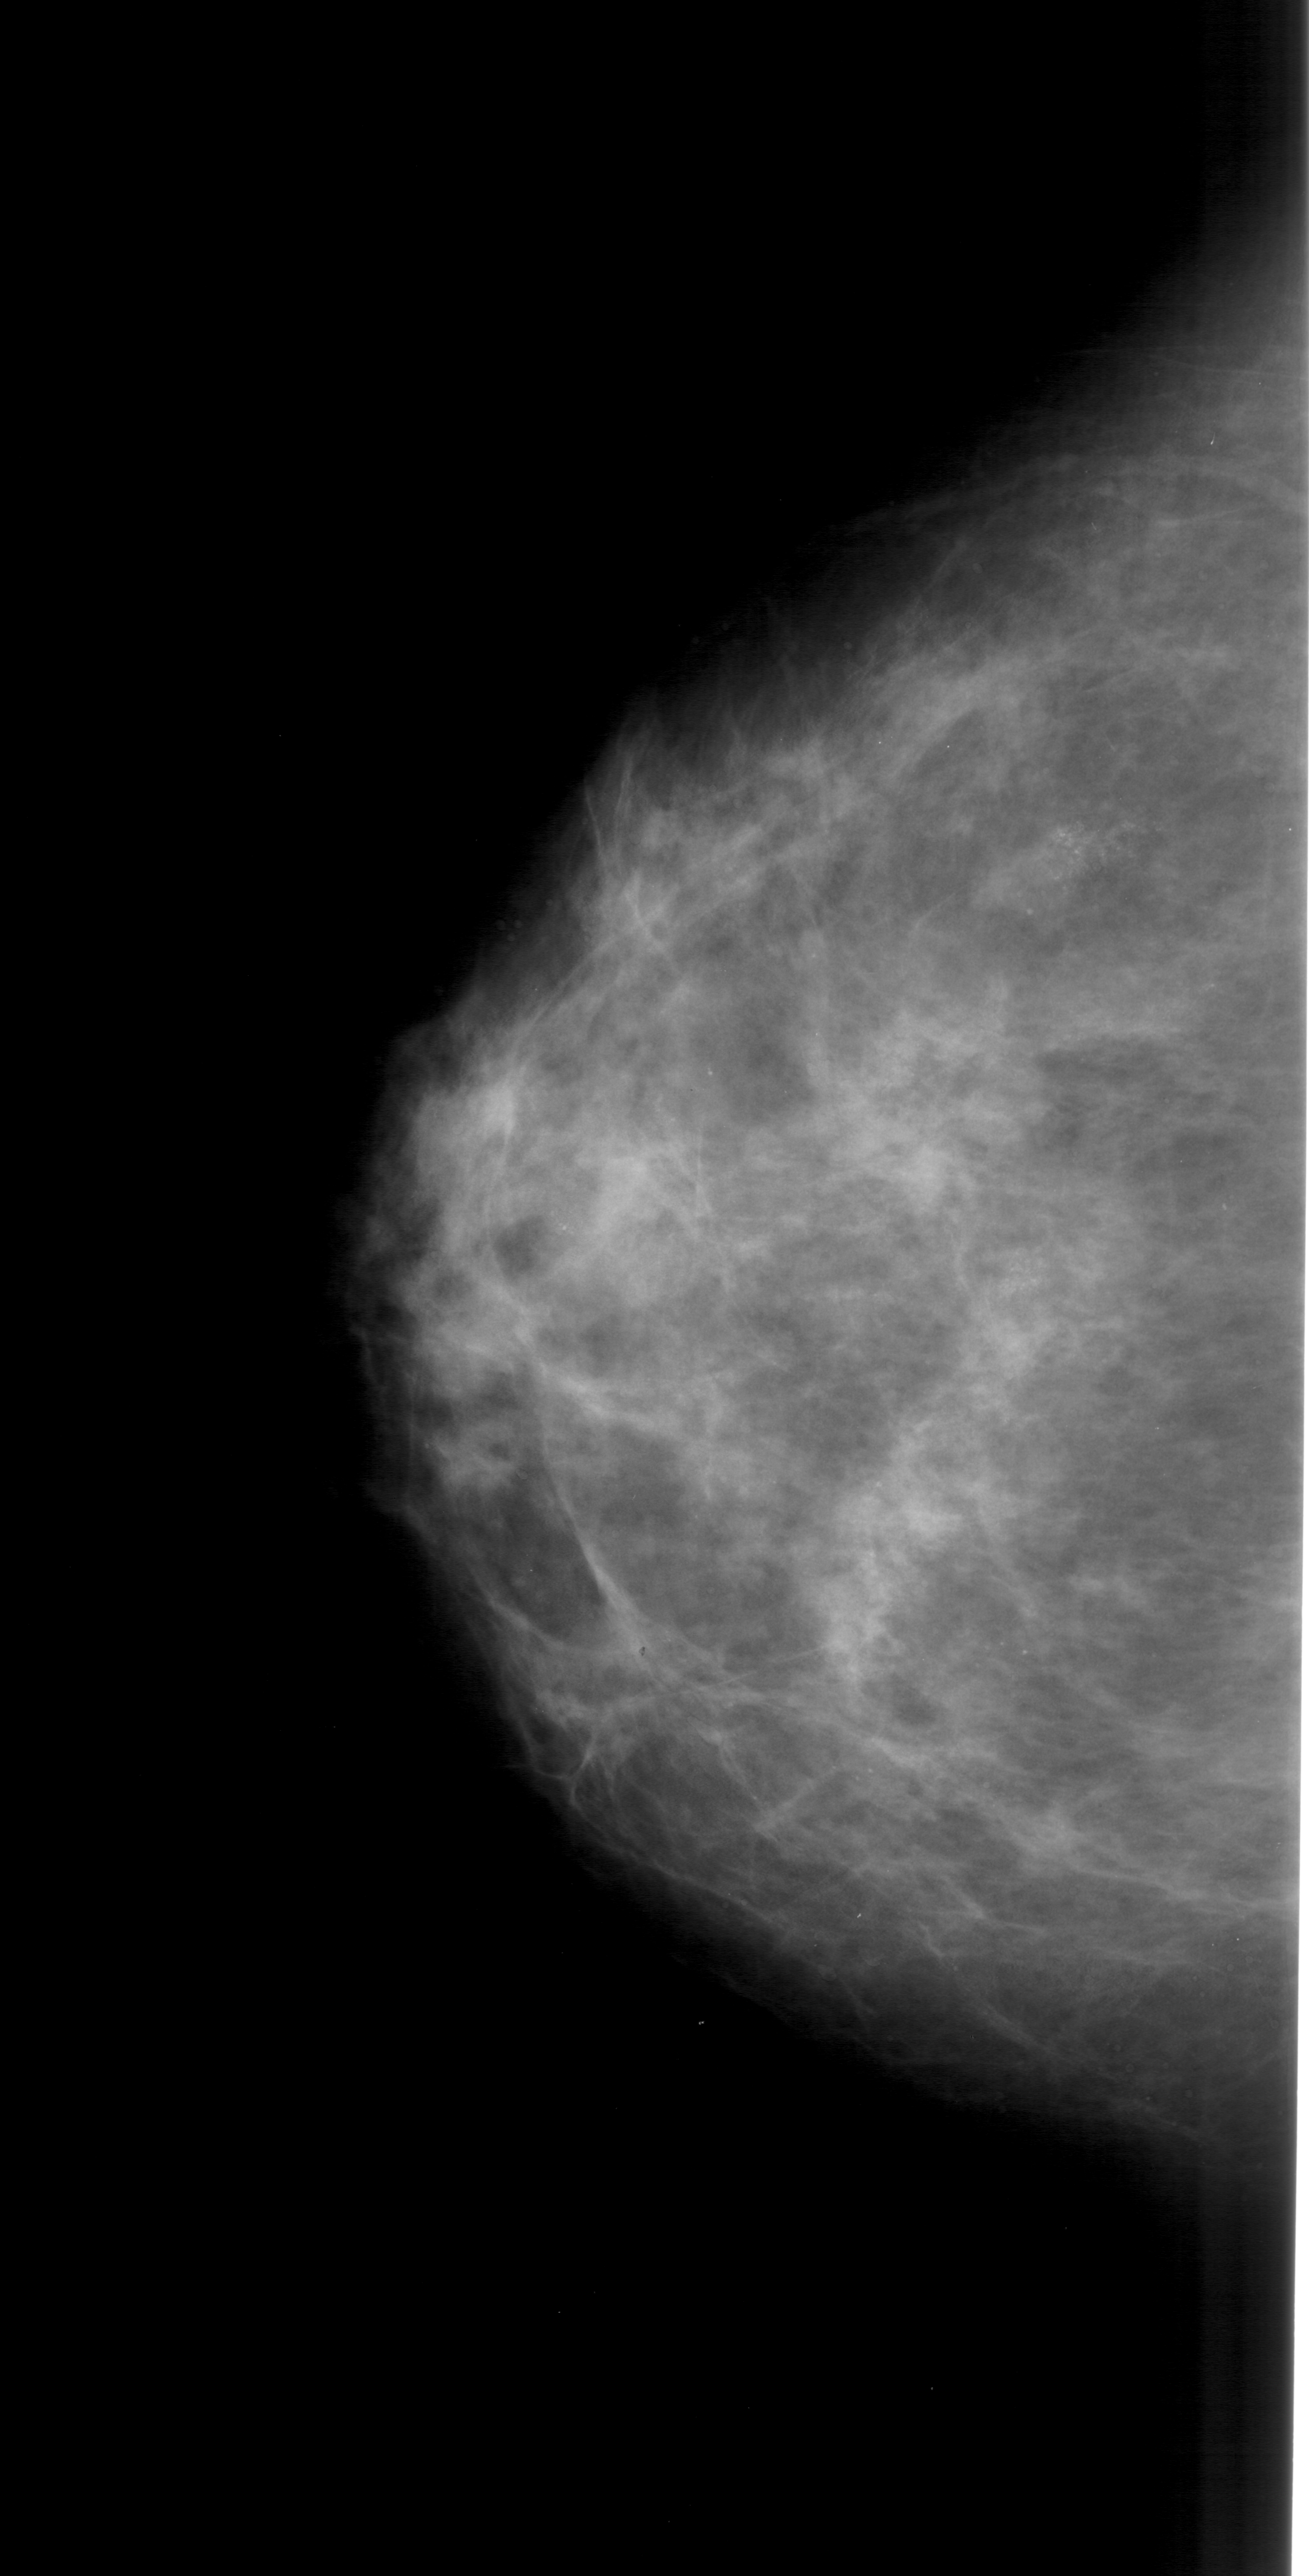
Digitized screen-film mammogram. Left breast. Craniocaudal (CC) view. Breast composition: heterogeneously dense (BI-RADS density category 3 of 4). 1309 × 2576 image matrix.
Expert-marked regions of interest on this film, with their recorded descriptors:
- calcifications, morphology pleomorphic, distribution clustered; BI-RADS assessment category 4; subtlety rating 3 on a 1 (subtle) to 5 (obvious) scale; pathology result (as recorded, not read from the image): malignant: bounding box <1029,799,1169,899> (left, top, right, bottom; pixels)